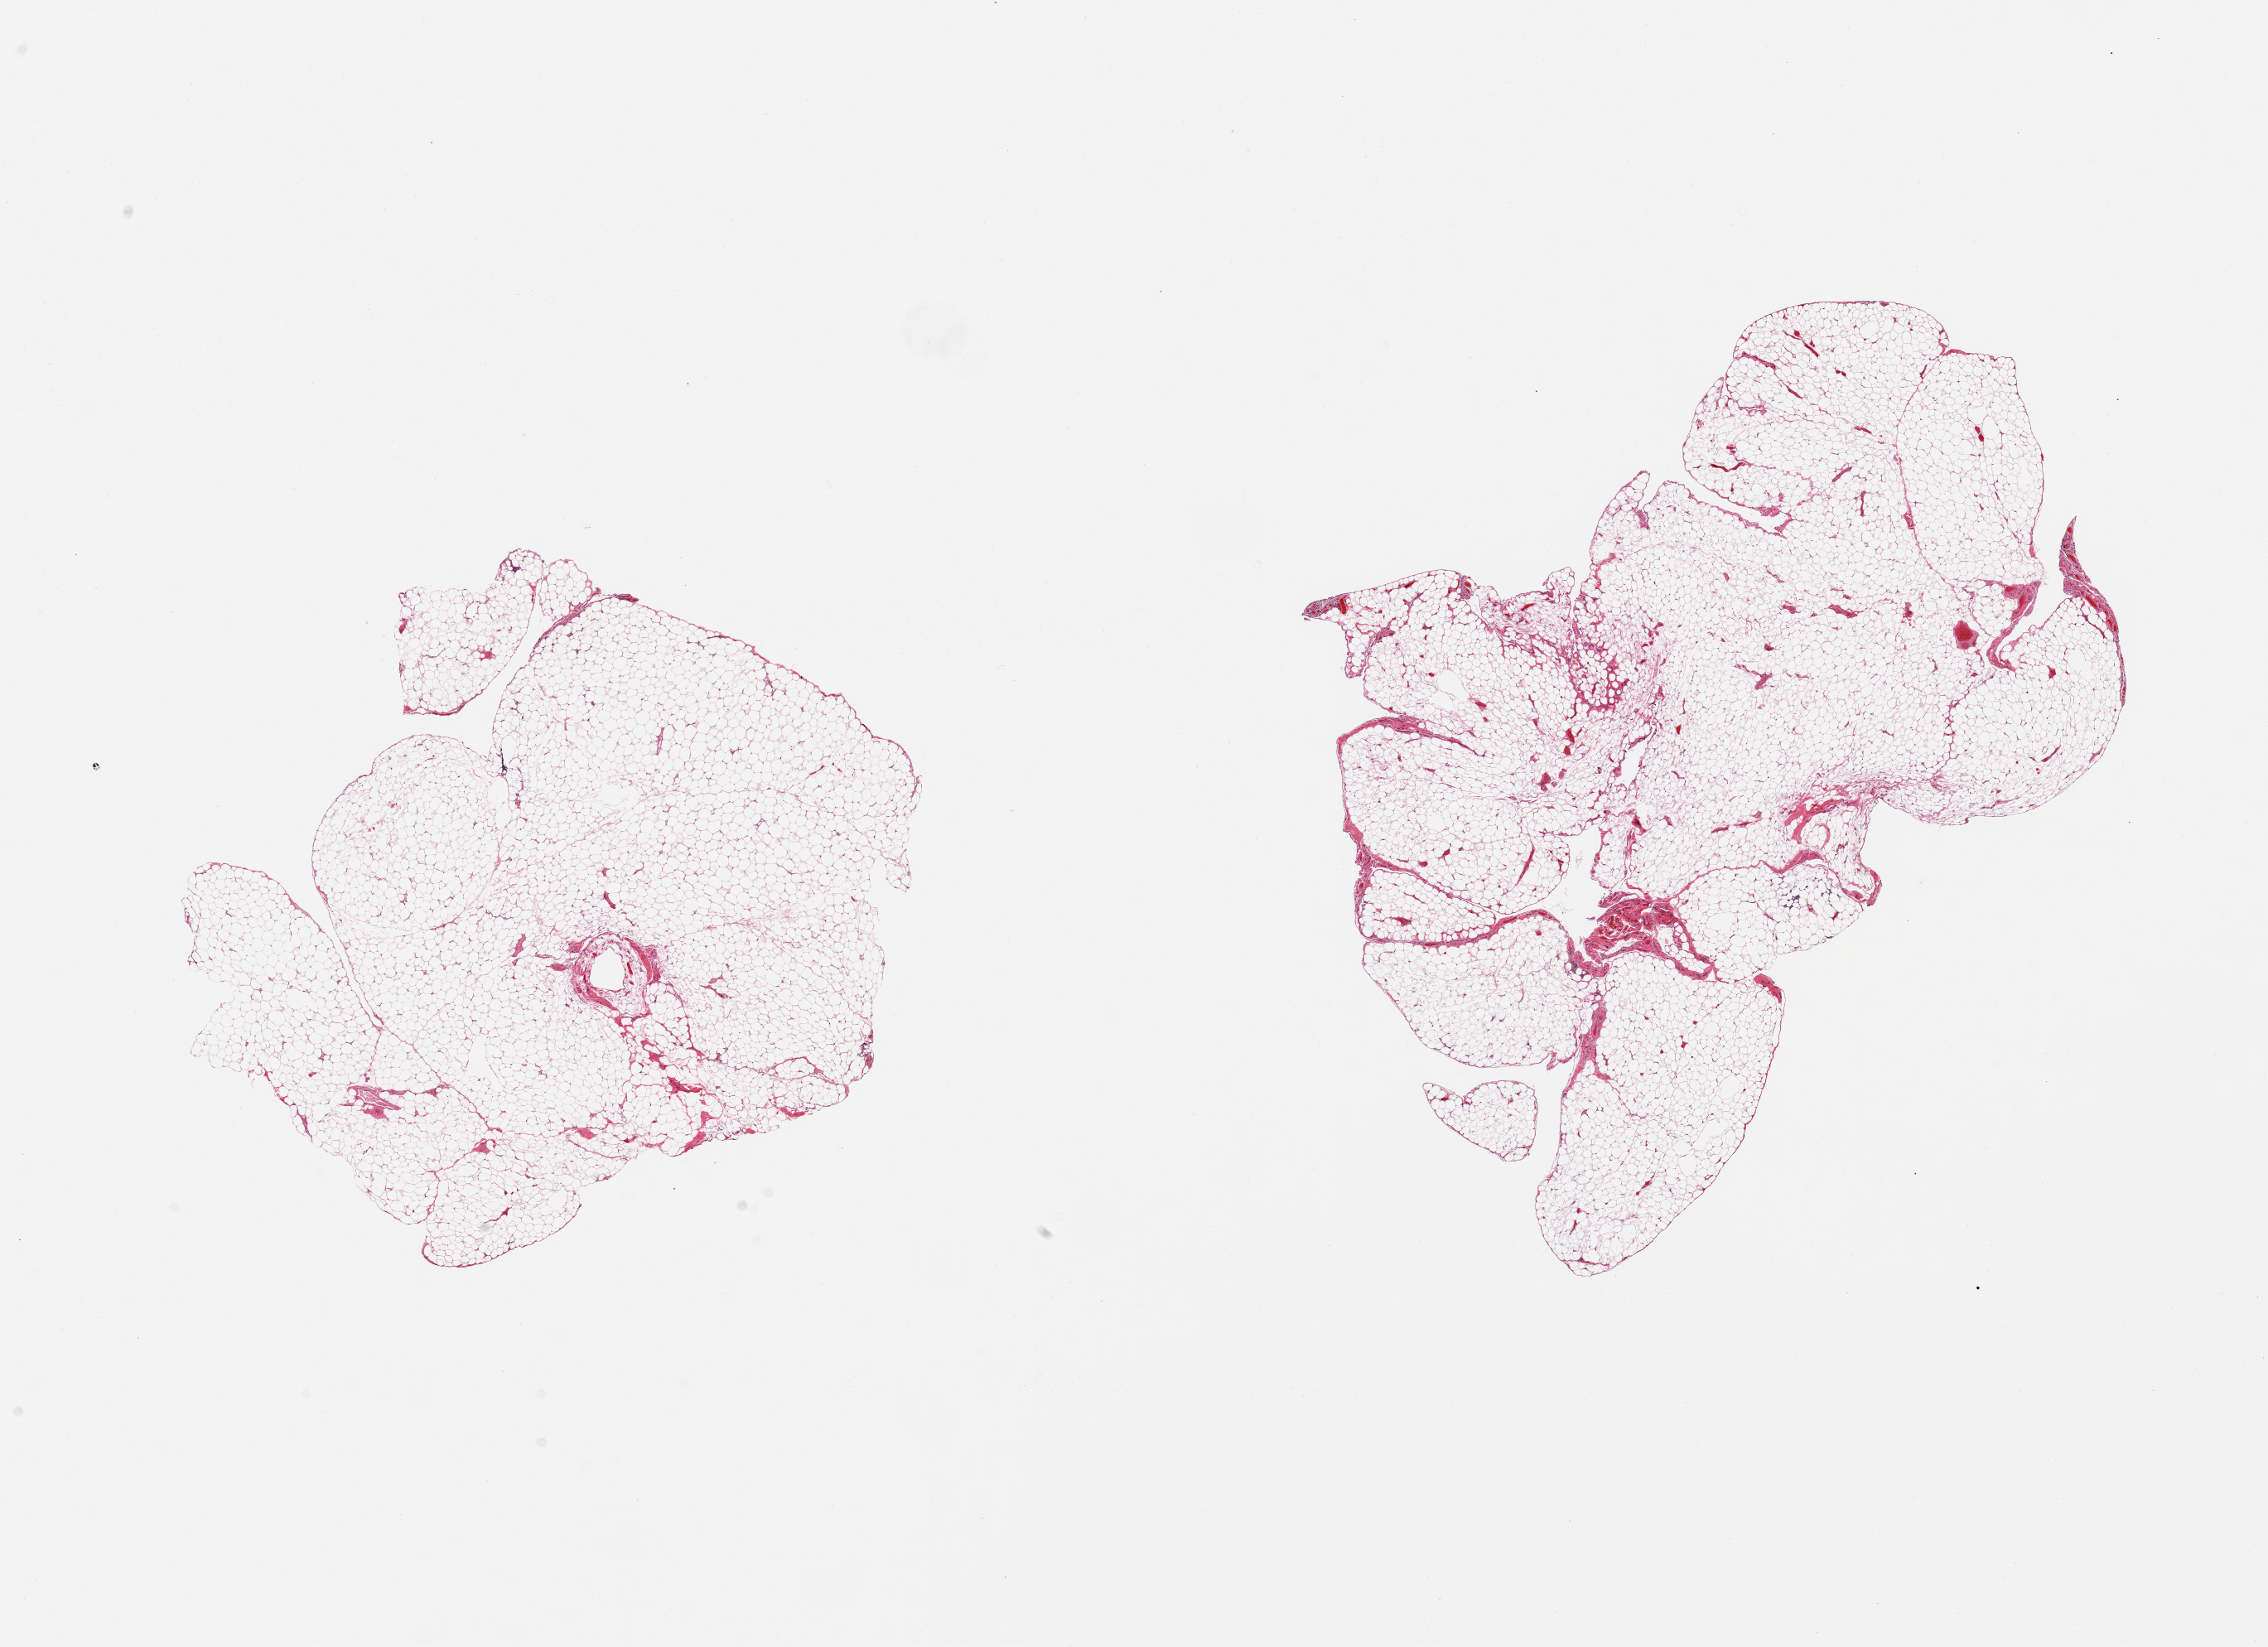
Whole-slide image, H&E stain, low-resolution overview of the scanned area, about 21.7 x 15.7 mm (acquisition: 20x scan). PAXgene-fixed paraffin-embedded (PFPE) section. Target tissue: omentum. Tissue donor sample. Donor: male.
Review note (as recorded): 2 pieces; <5% fibrous content.